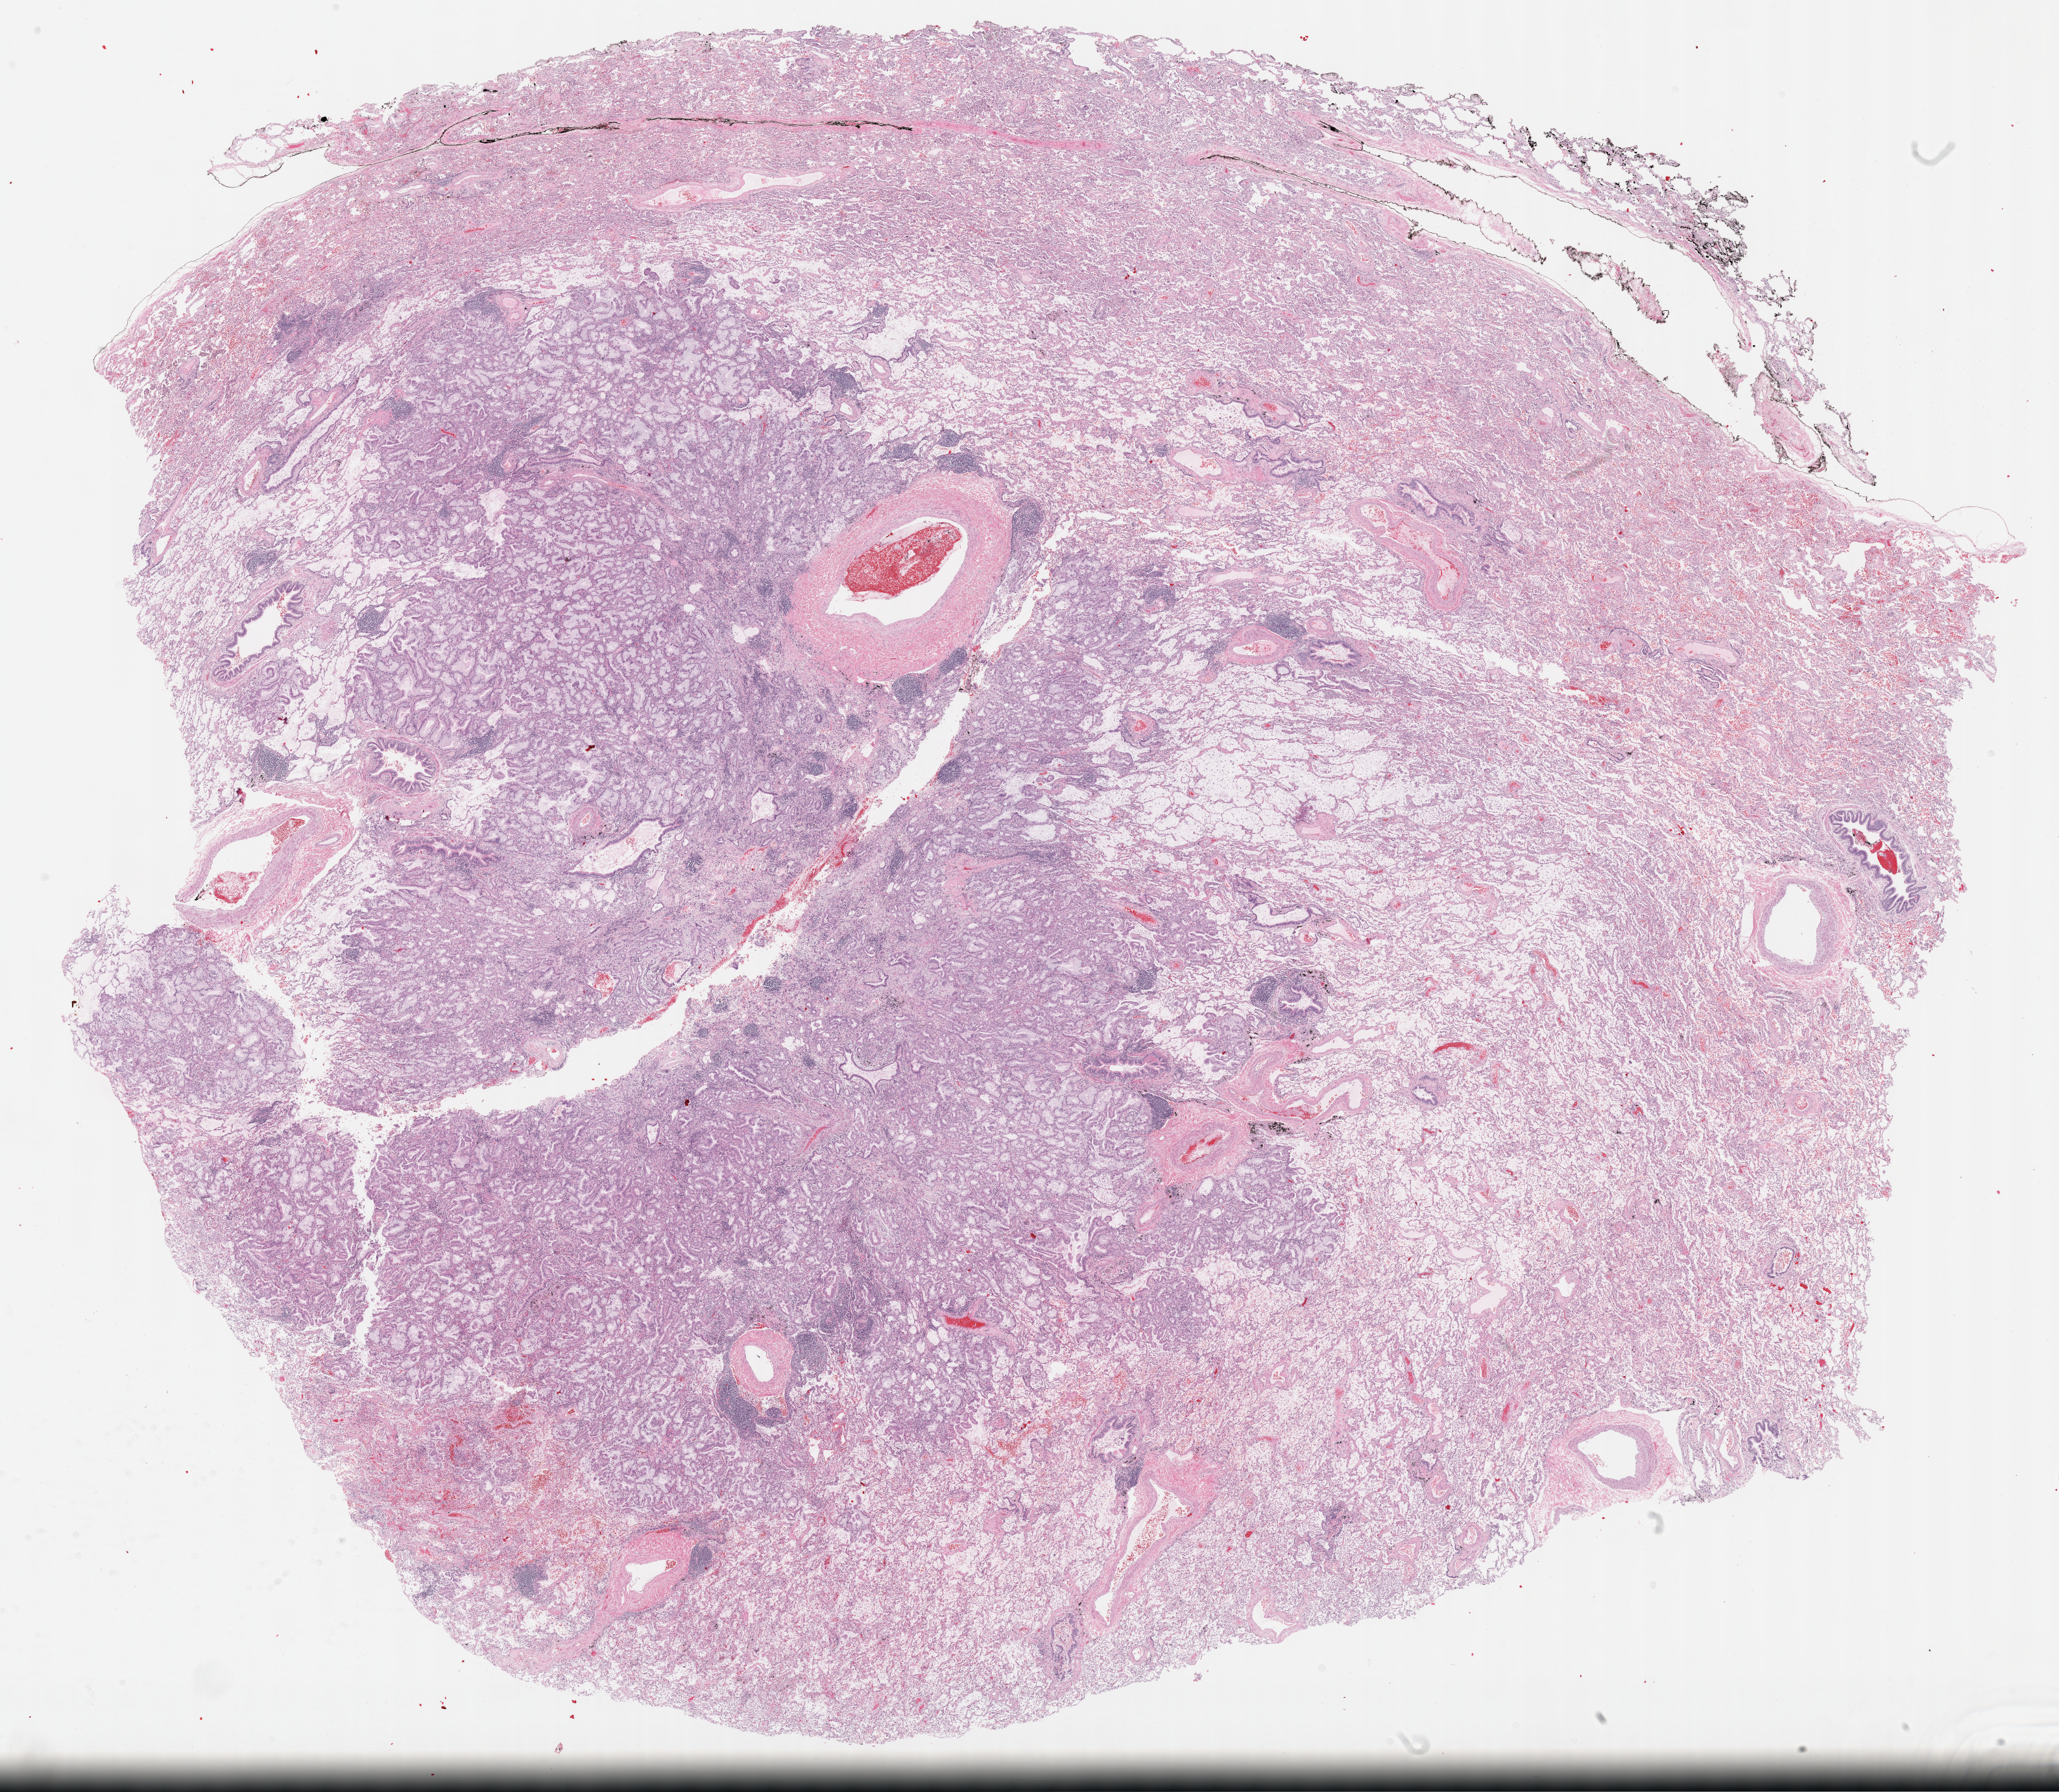
Whole-slide histology image, H&E, low-resolution overview of the scanned area, about 25.7 x 22.3 mm, formalin-fixed paraffin-embedded (FFPE) diagnostic section, sample: primary tumour, lung. Female patient; age at initial diagnosis 68 years.
Histologic diagnosis: Bronchio-alveolar carcinoma, mucinous (upper lobe, lung). Laterality: right. AJCC pathologic stage: IA (7th edition).